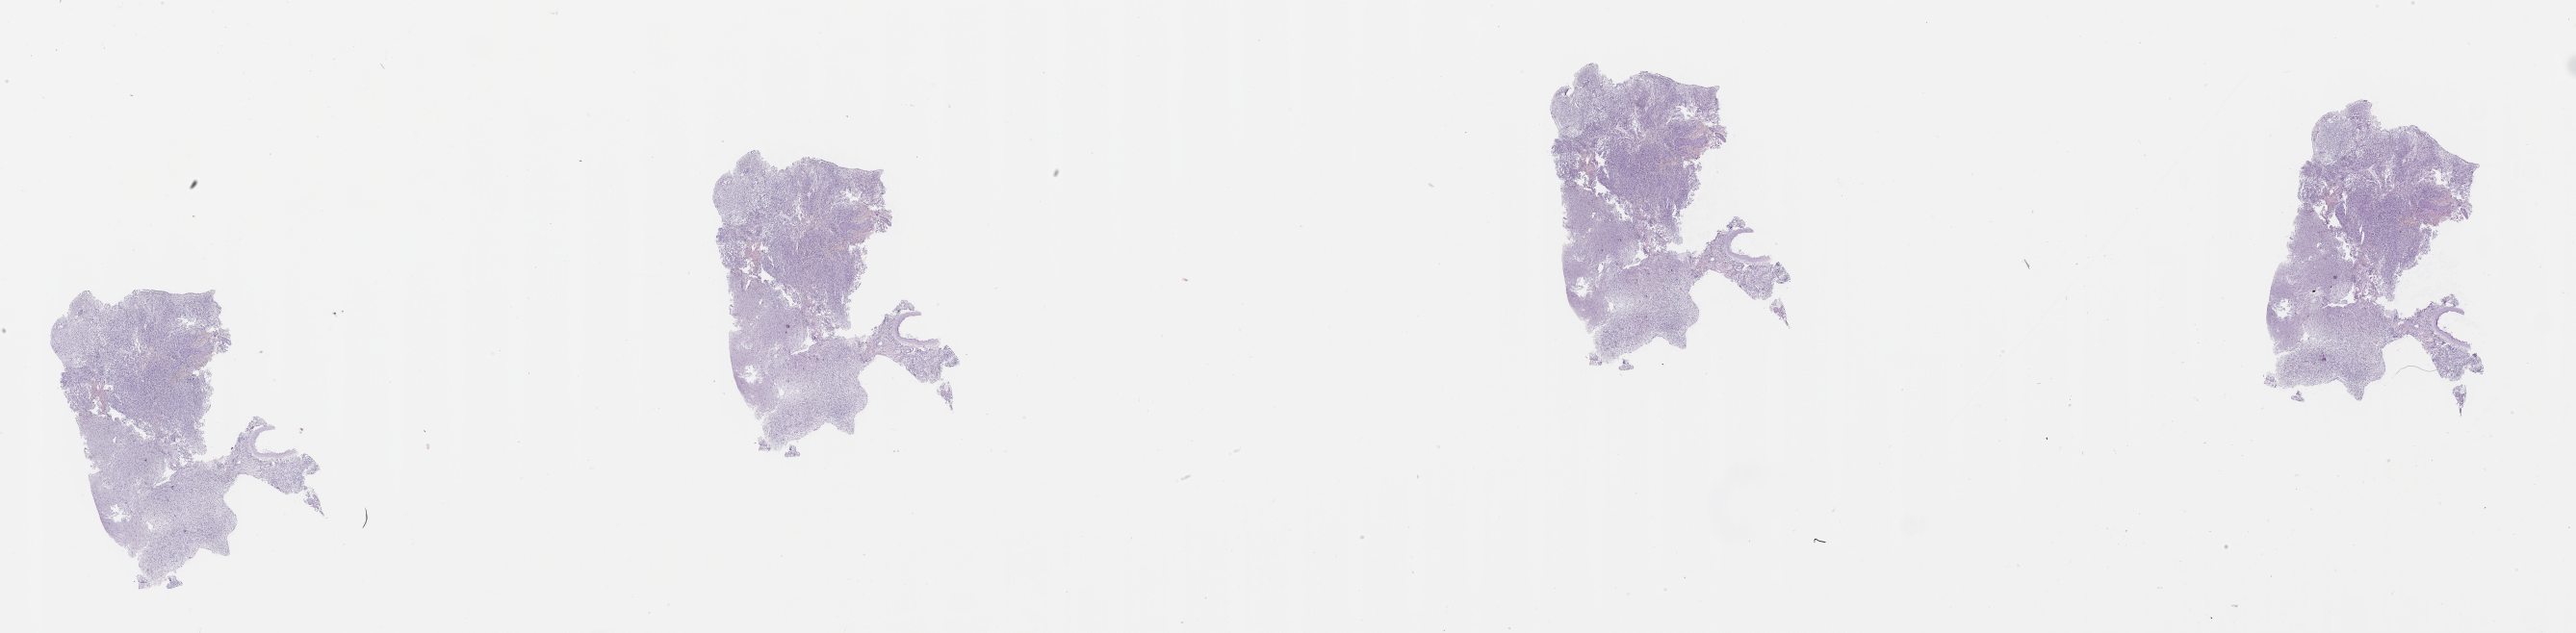
H&E-stained whole-slide image — low-resolution overview of the scanned area, about 43.1 x 10.6 mm; tumour tissue sample, sampled site: brain. Patient: female, age 81 years. Composition of this section per pathologist review: tumour nuclei 70%, necrosis 5%.
Diagnosis: Glioblastoma. Primary tumour site (as recorded): parietal lobe.